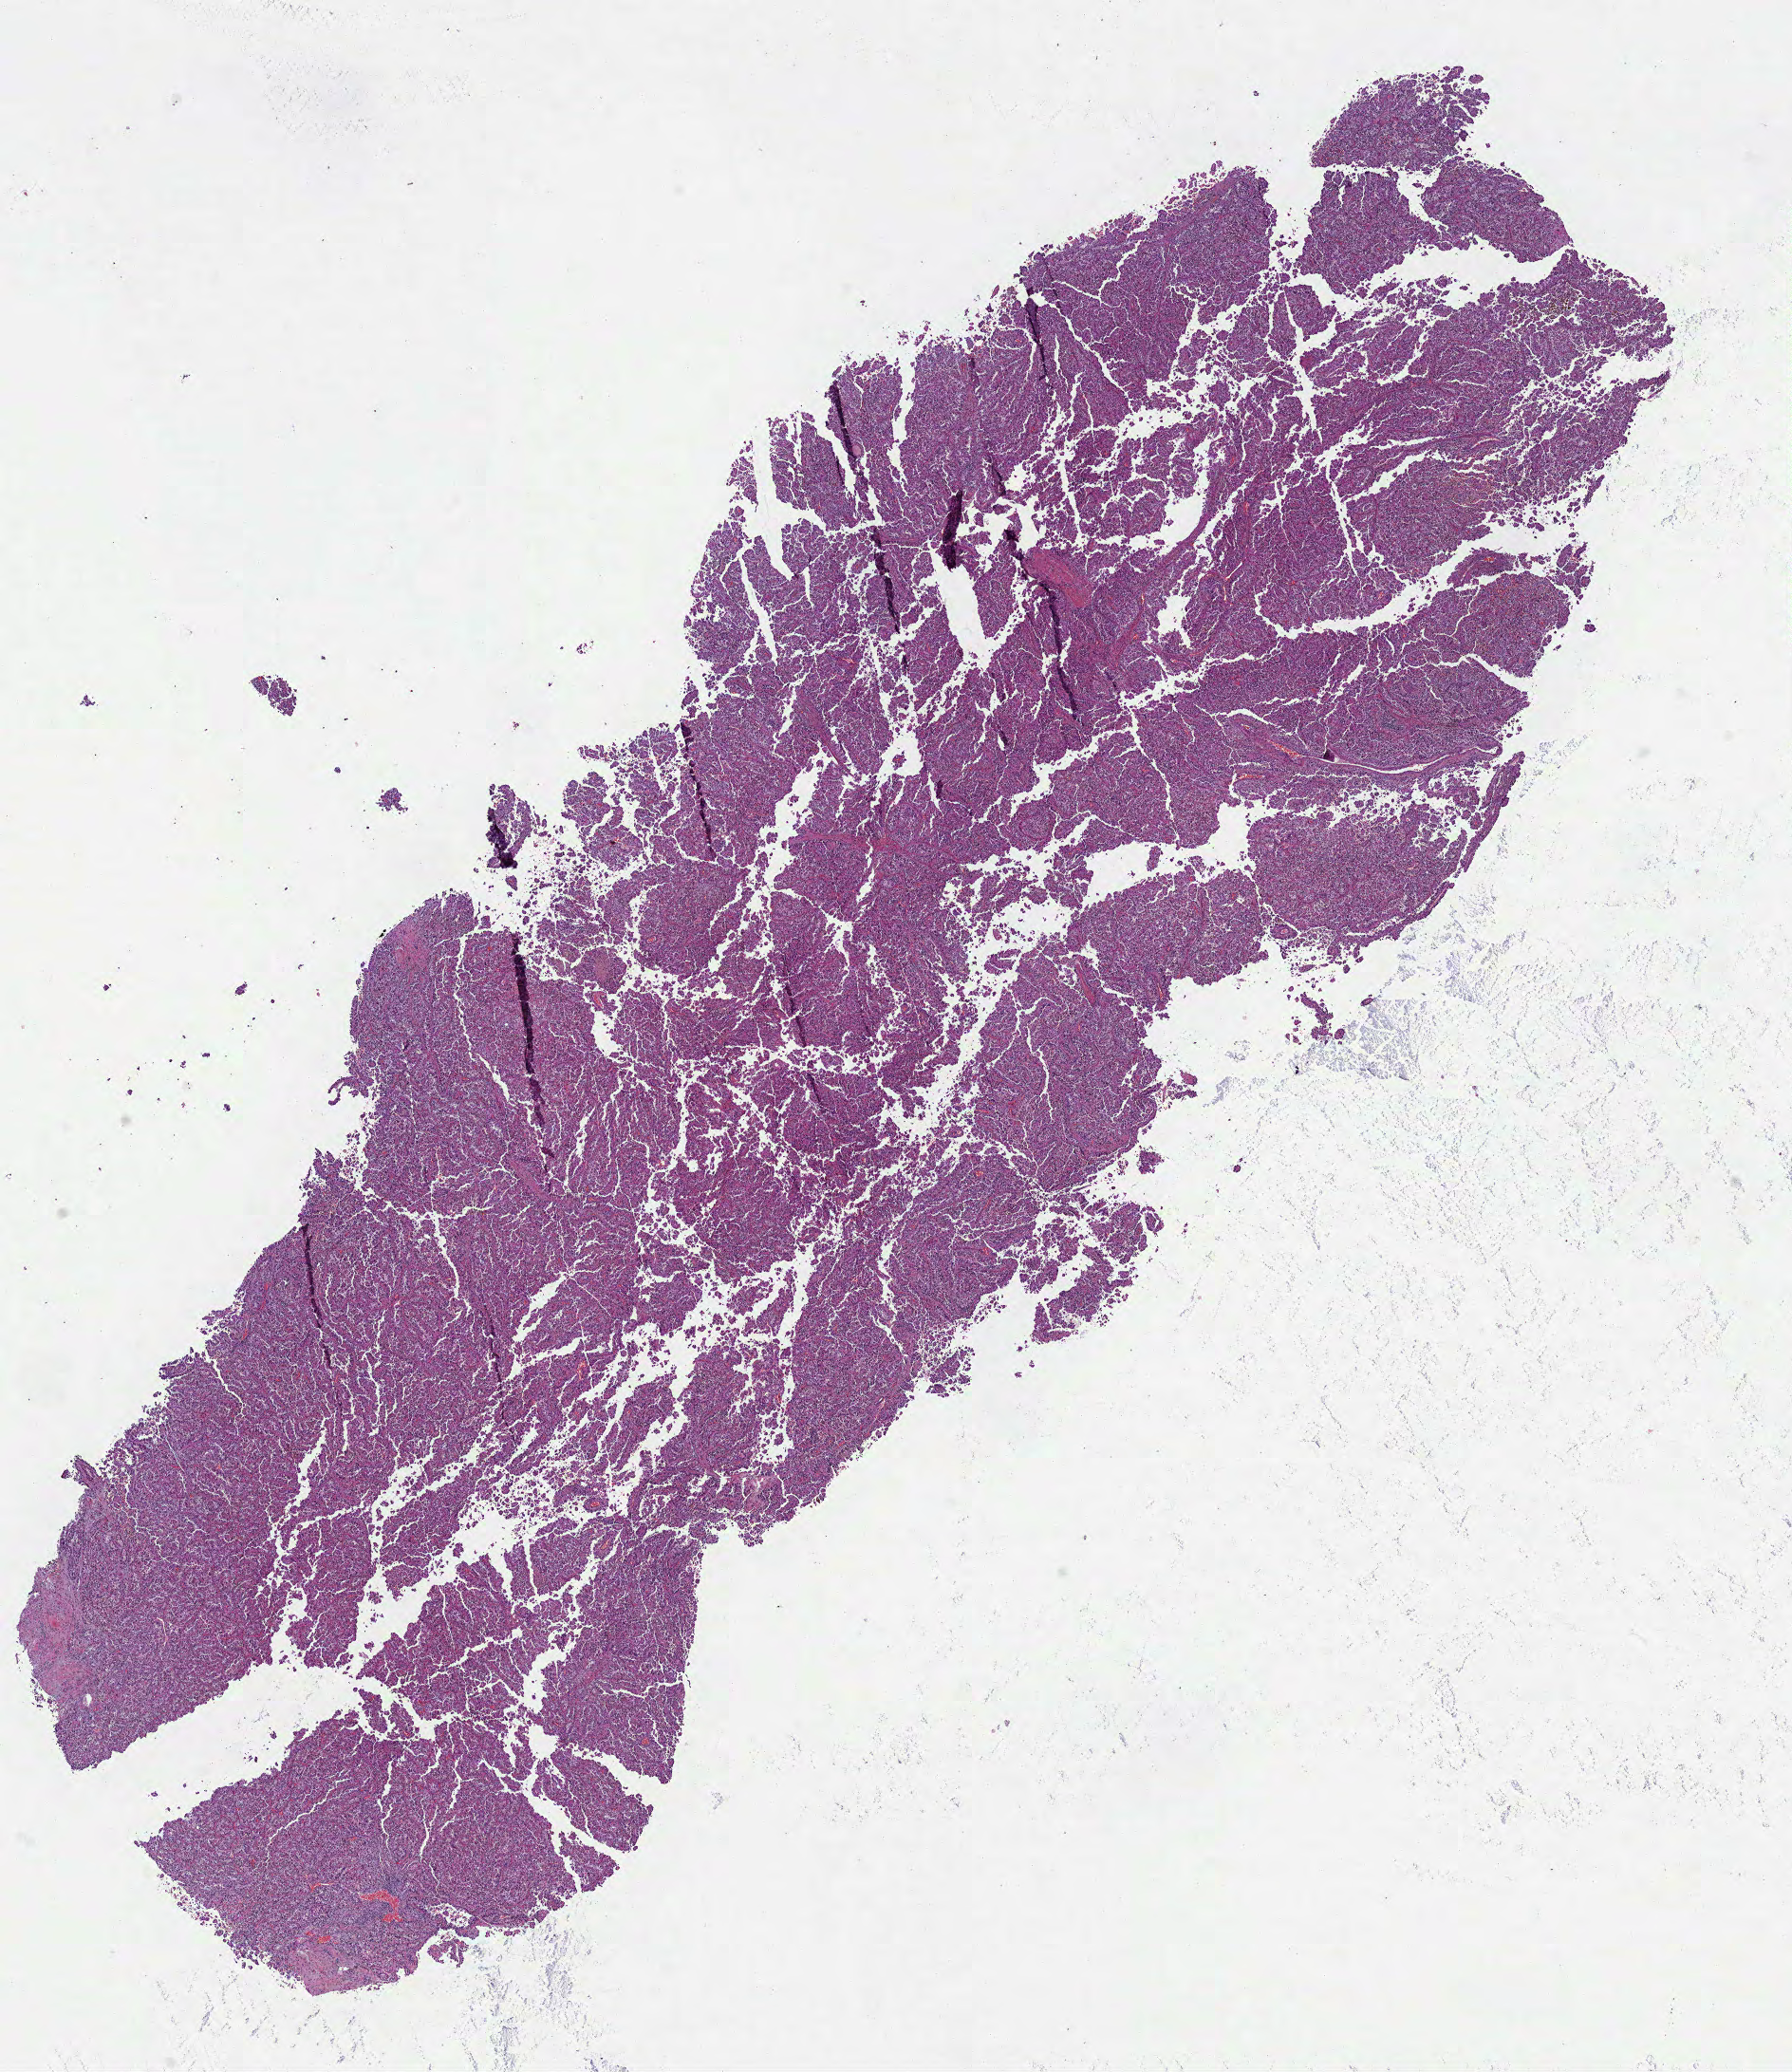
H&E-stained whole-slide image, shown as a low-resolution overview of the whole scanned area (about 15.2 x 17.6 mm, slide scanned at 40x), FFPE section, sample: primary tumour, kidney. Male patient; age at initial diagnosis 59 years.
* AJCC pathologic stage: IV (7th edition)
* lymph nodes positive (case pathology): 0 of 1 examined
* histologic diagnosis: Papillary adenocarcinoma, NOS